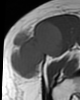
MRI of an extremity soft-tissue mass, one axial slice. Slice 21 of 46 in the series (ordered by position). MR volume resampled by the dataset authors to the PET/CT grid (not the native acquisition matrix). 3.27 mm slice thickness. 80 × 100 image matrix, field of view 78 × 98 mm. Female patient. Case-level facts recorded for this patient, not image findings: histological type: synovial sarcoma; grade: intermediate; site of the primary tumour: right thigh.
Structures marked on this image (expert contour drawn on MRI and transferred to this co-registered scan by the dataset authors):
- gross tumour volume including surrounding oedema: box from (x=10, y=21) to (x=63, y=79) px
- gross tumour volume (mass): (x=10, y=21)–(x=63, y=79)